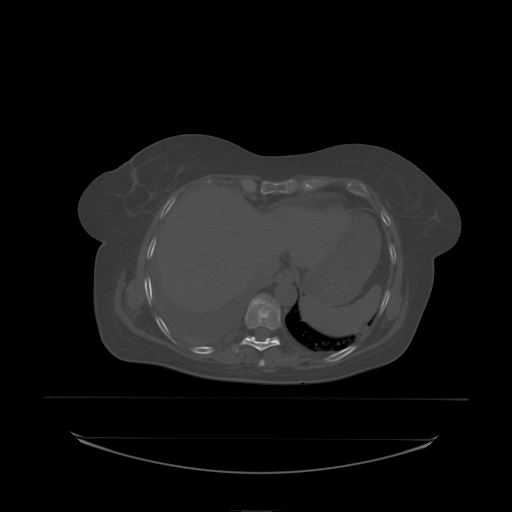
CT including the spine, one axial slice. Position 122 of 242 along the scan axis. Bone window (W 1800 / L 400 HU). 512 × 512 image matrix, field of view 500 × 500 mm. Patient: female, 53 years. From the clinical record (not read from this slice): primary cancer: lung; vertebrae with lytic lesions (as recorded): T7, L1.
Annotated regions visible in this slice (semi-automatically segmented with operator editing):
- T10 vertebra: box from (x=249, y=337) to (x=255, y=338) px
- T9 vertebra: (x=246, y=296)–(x=281, y=330)